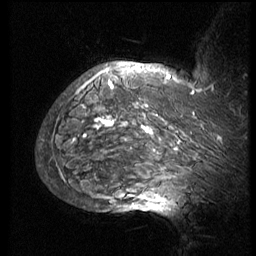
Breast MRI (dynamic contrast-enhanced), one sagittal slice; position 58 of 74 along the scan axis; 3 images stored at this slice position (order not interpretable as contrast timing); 1.5 T; TE 4.2 ms, TR 8.9 ms; 2.5 mm slice thickness; 256 × 256 image matrix, field of view 200 × 200 mm. Patient: female, 57 years. From the clinical record (not read from this slice): setting: breast cancer imaged before/during neoadjuvant chemotherapy; receptor status: HER2-positive.
Annotated regions visible in this slice (semi-automatic segmentation, software-assisted and operator-edited):
- analysis volume of interest (the breast-tissue region the enhancement analysis was run in; not a lesion): bounding box [x1, y1, x2, y2] px = [51, 67, 248, 173]
- tumour enhancement mask (voxels above the 140 % enhancement threshold inside the analysis volume of interest): [74, 71, 201, 141]